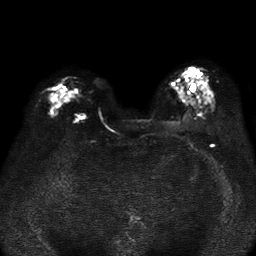
Breast MRI, one axial slice. Position 20 of 37 along the scan axis. Diffusion-weighted series; image 2 of 4 stored at this slice position (different b-values; order by instance number). 1.5 T. 5 mm slice thickness. 256 × 256 image matrix. Female patient.
Annotated regions visible in this slice (manually delineated by an expert):
- tumour on diffusion-weighted imaging: box from (x=66, y=89) to (x=74, y=98) px